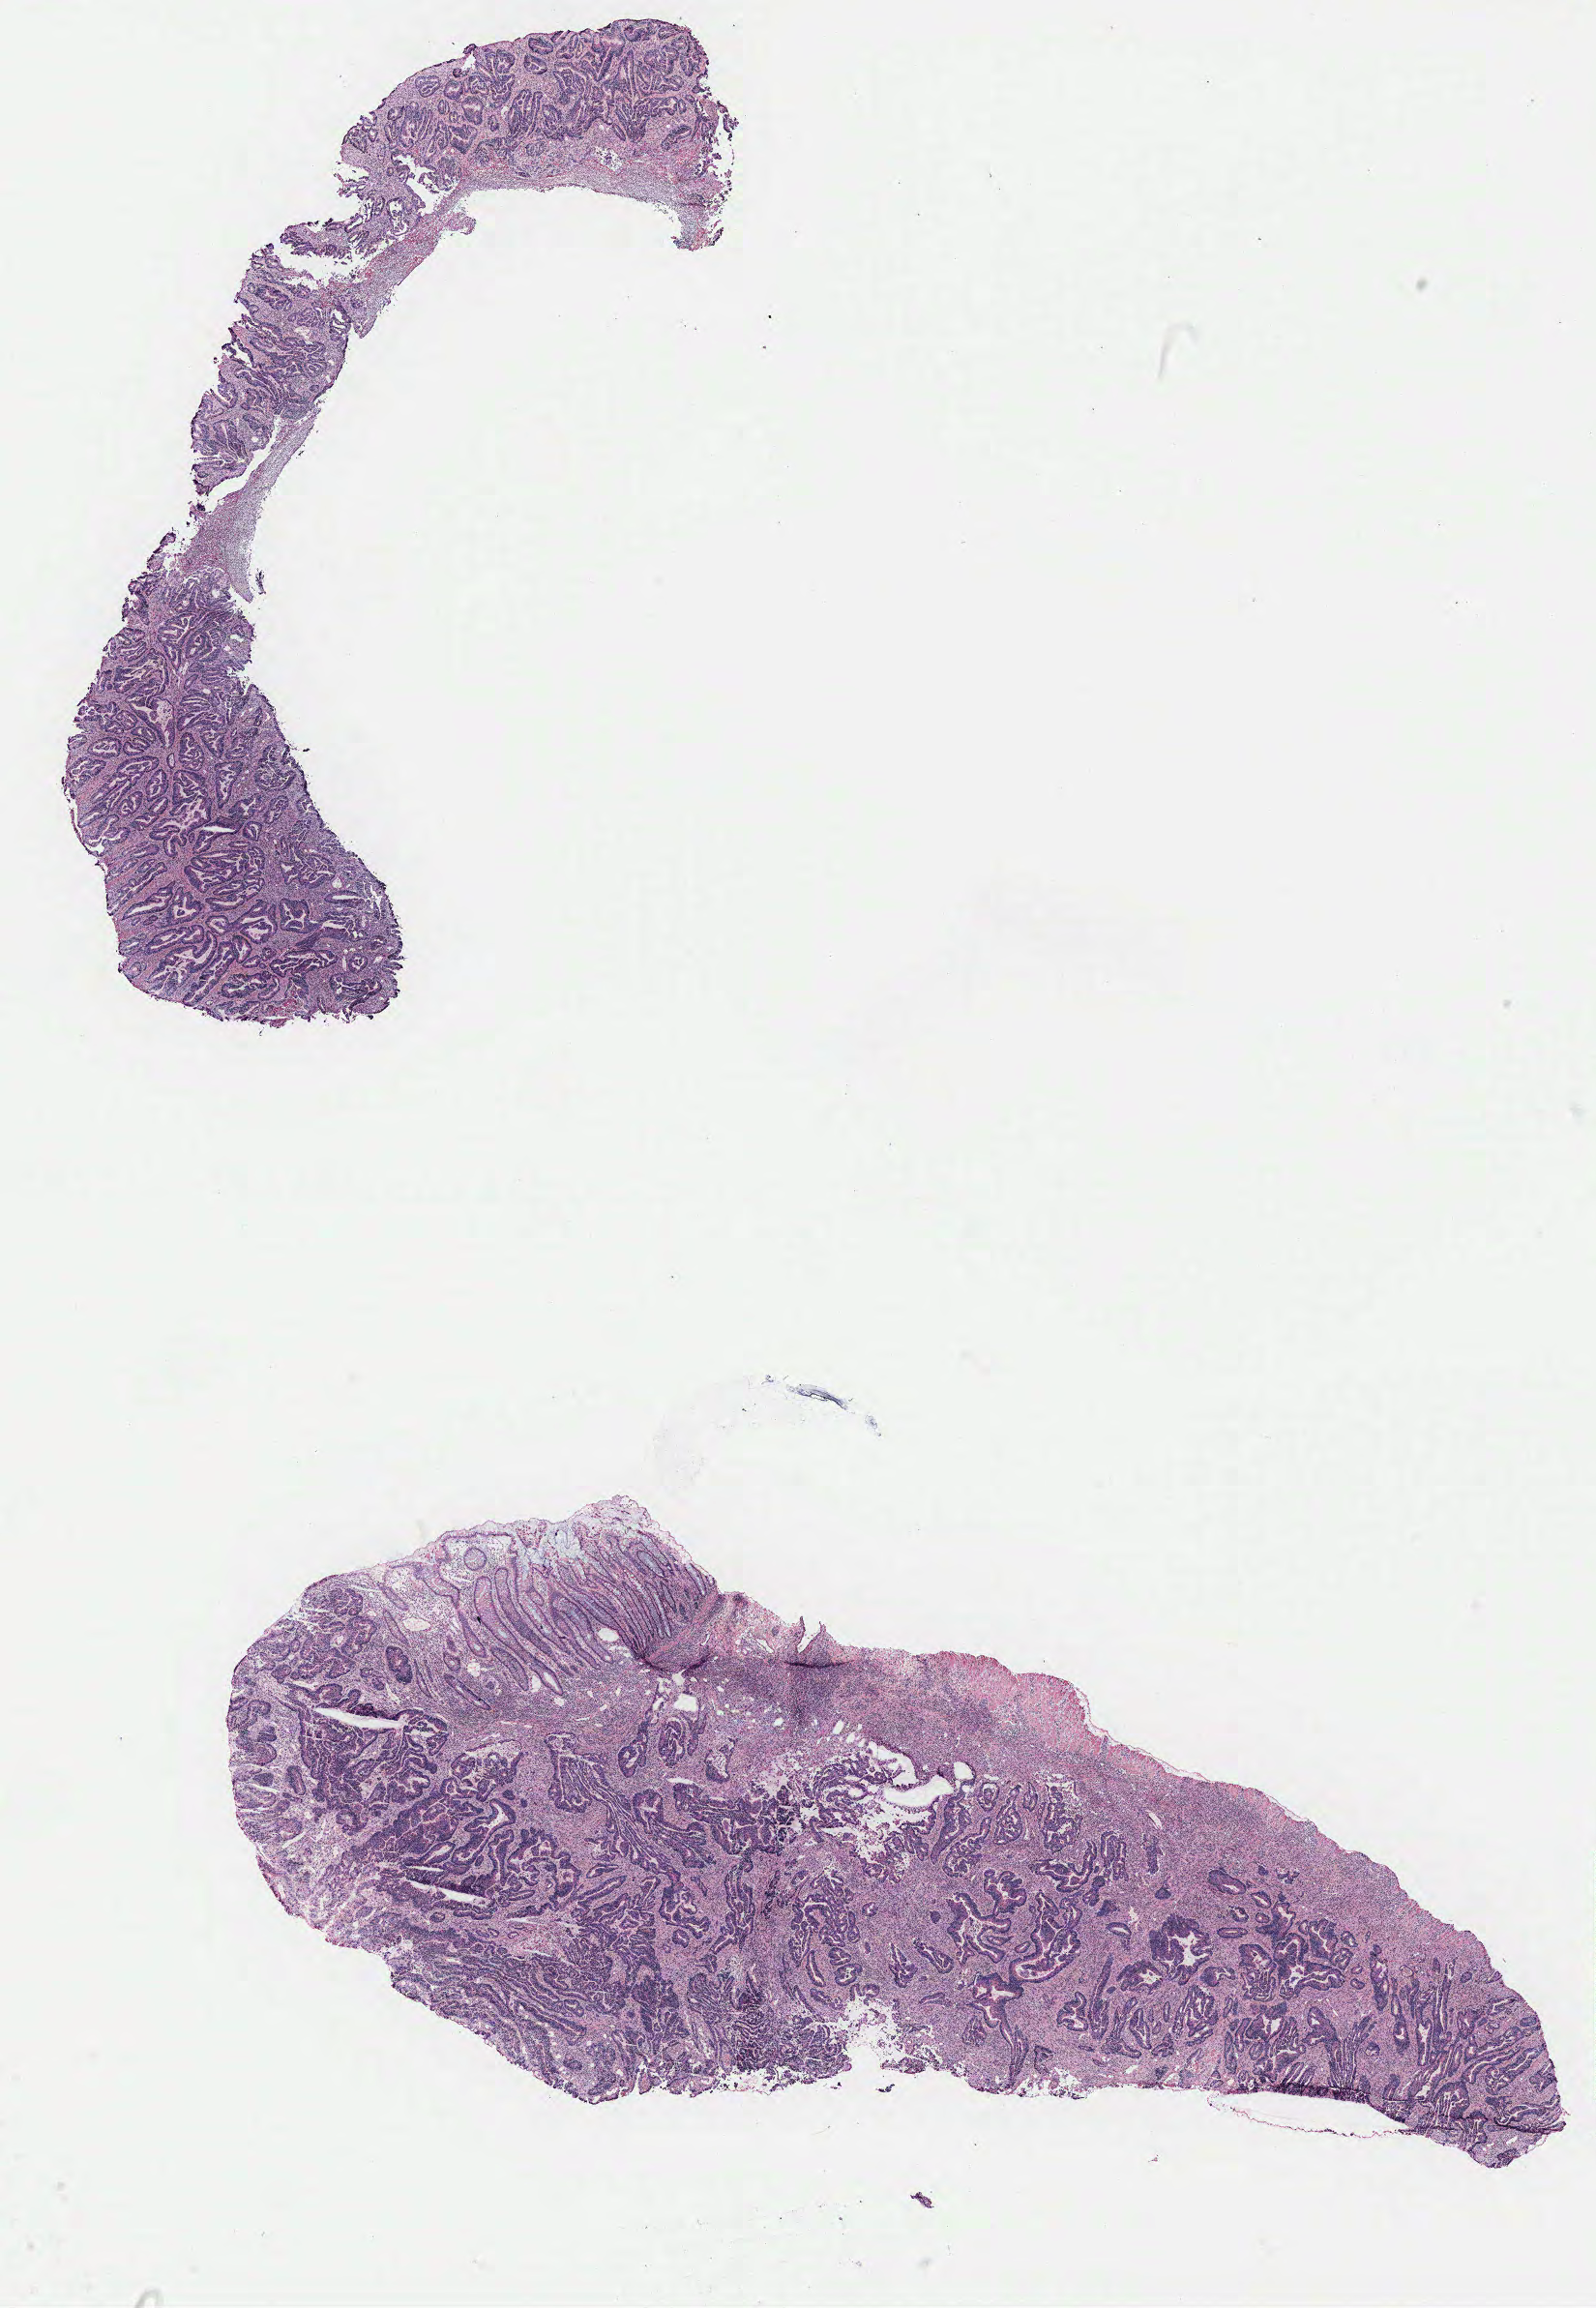
Whole-slide histology image, Hematoxylin and eosin (H&E) stained — a low-resolution overview of the entire scanned area, about 13.2 x 19.1 mm (acquisition: 40x scan), colon, tissue type not recorded.
• patient diagnosis (cohort enrolment): colon cancer (colon)